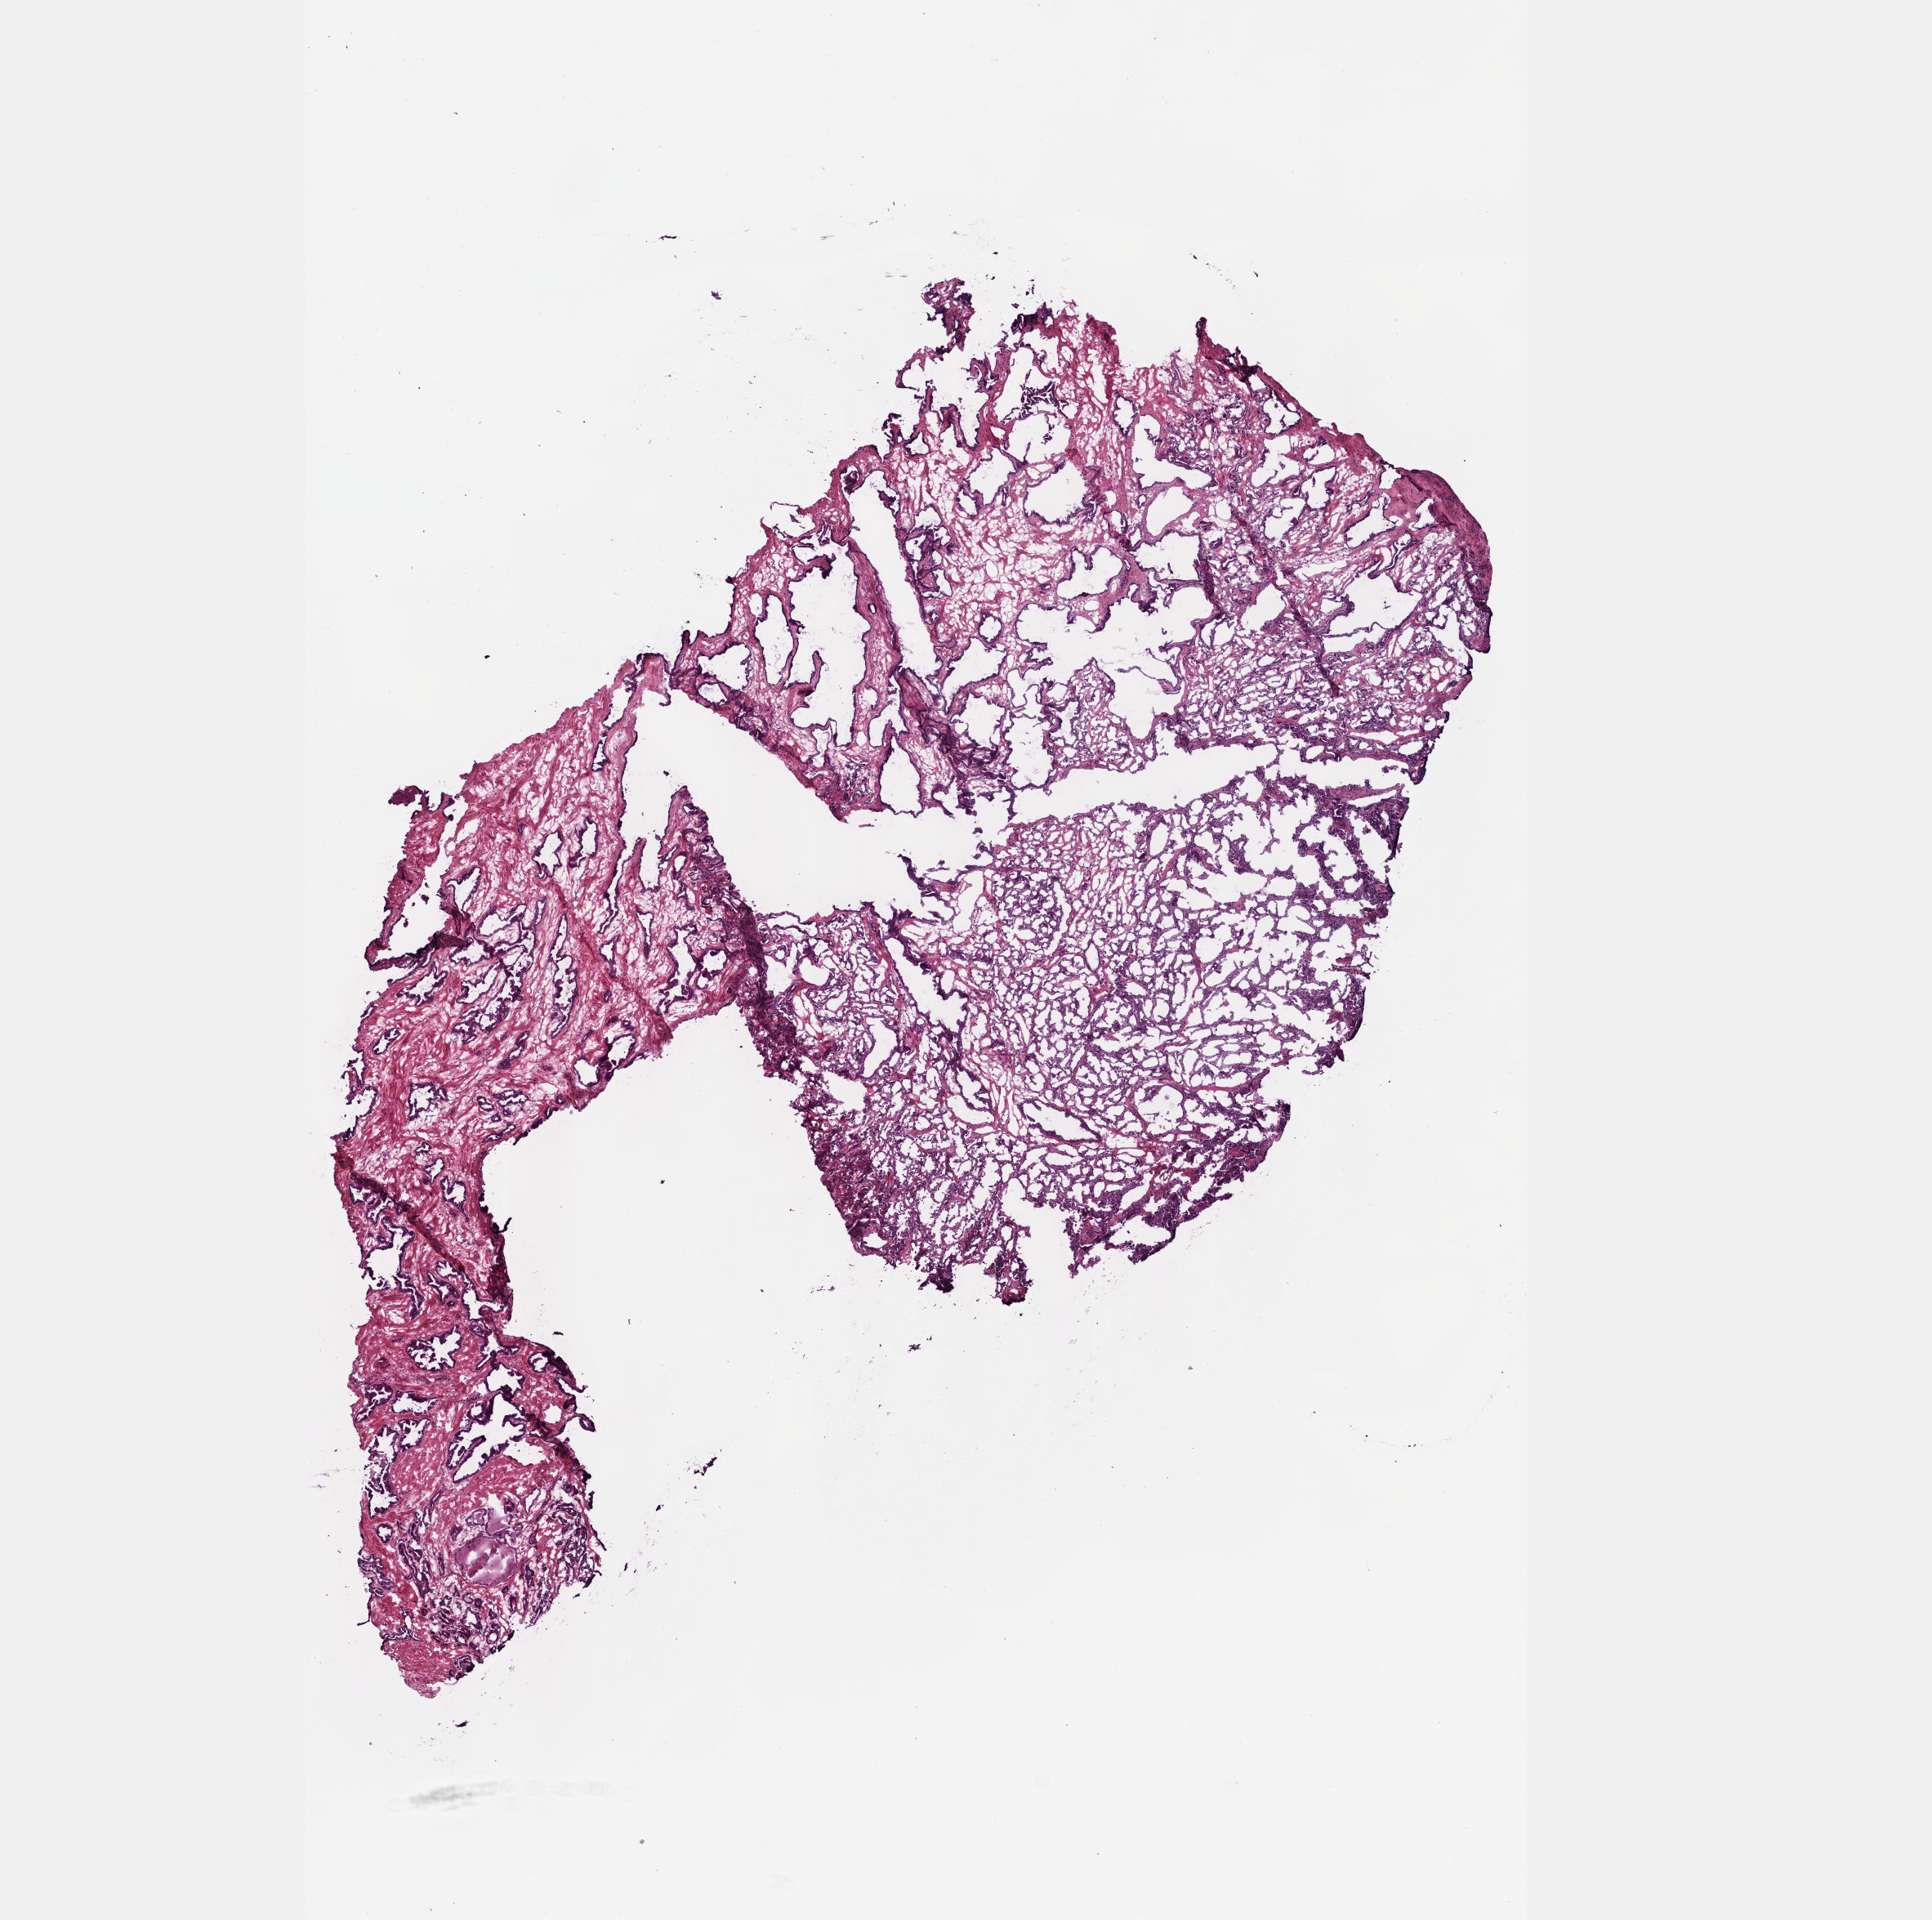
H&E whole-slide image — a low-resolution overview of the entire scanned area, about 9.6 x 9.5 mm (slide scanned at 40x). Frozen section from the bottom of the tissue portion. Sample: primary tumour, prostate. Male patient; age at initial diagnosis 66 years. Gleason score: 7 (4+3).
- lymph nodes positive (case pathology): 0 of 13 examined
- diagnosis: Acinar cell carcinoma (prostate gland)